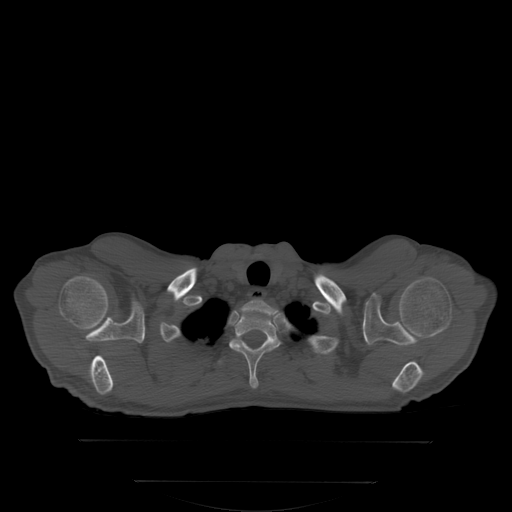
CT including the spine, one axial slice; position 287 of 350 along the scan axis; bone window (W 1800 / L 400 HU); 512 × 512 image matrix, field of view 500 × 500 mm. Patient: male, 58 years. Case-level facts recorded for this patient, not image findings: primary cancer: prostate; vertebrae with lytic lesions (as recorded): L1.
Annotated regions visible in this slice (semi-automatically segmented with operator editing):
- T1 vertebra: box from (x=230, y=312) to (x=282, y=387) px